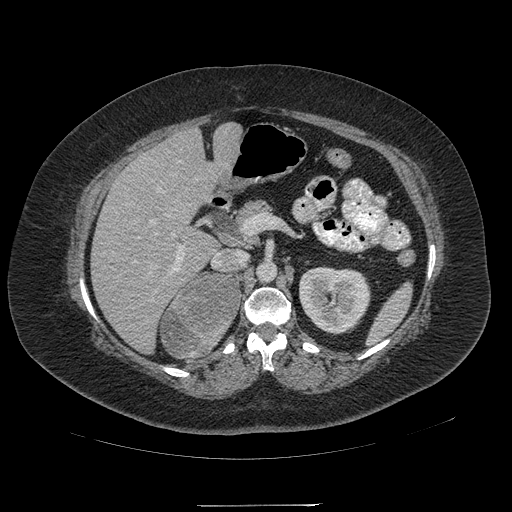
Contrast-enhanced abdominal CT, one axial slice; position 122 of 217 along the scan axis; reconstruction kernel STANDARD; 120 kVp; soft-tissue window (W 400 / L 40 HU); 1.25 mm slice thickness; 512 × 512 image matrix, field of view 453 × 453 mm. Female patient, age 55 years. From the clinical record (not read from this slice): diagnosis: adrenocortical carcinoma; tumour side: right adrenal; tumour size at pathology: 11 cm; Ki-67 index: 20 %; stage (as recorded): 2.
Structures marked on this image (semi-automatically segmented with operator editing):
- mass: bounding box <163,275,238,358> (left, top, right, bottom; pixels)